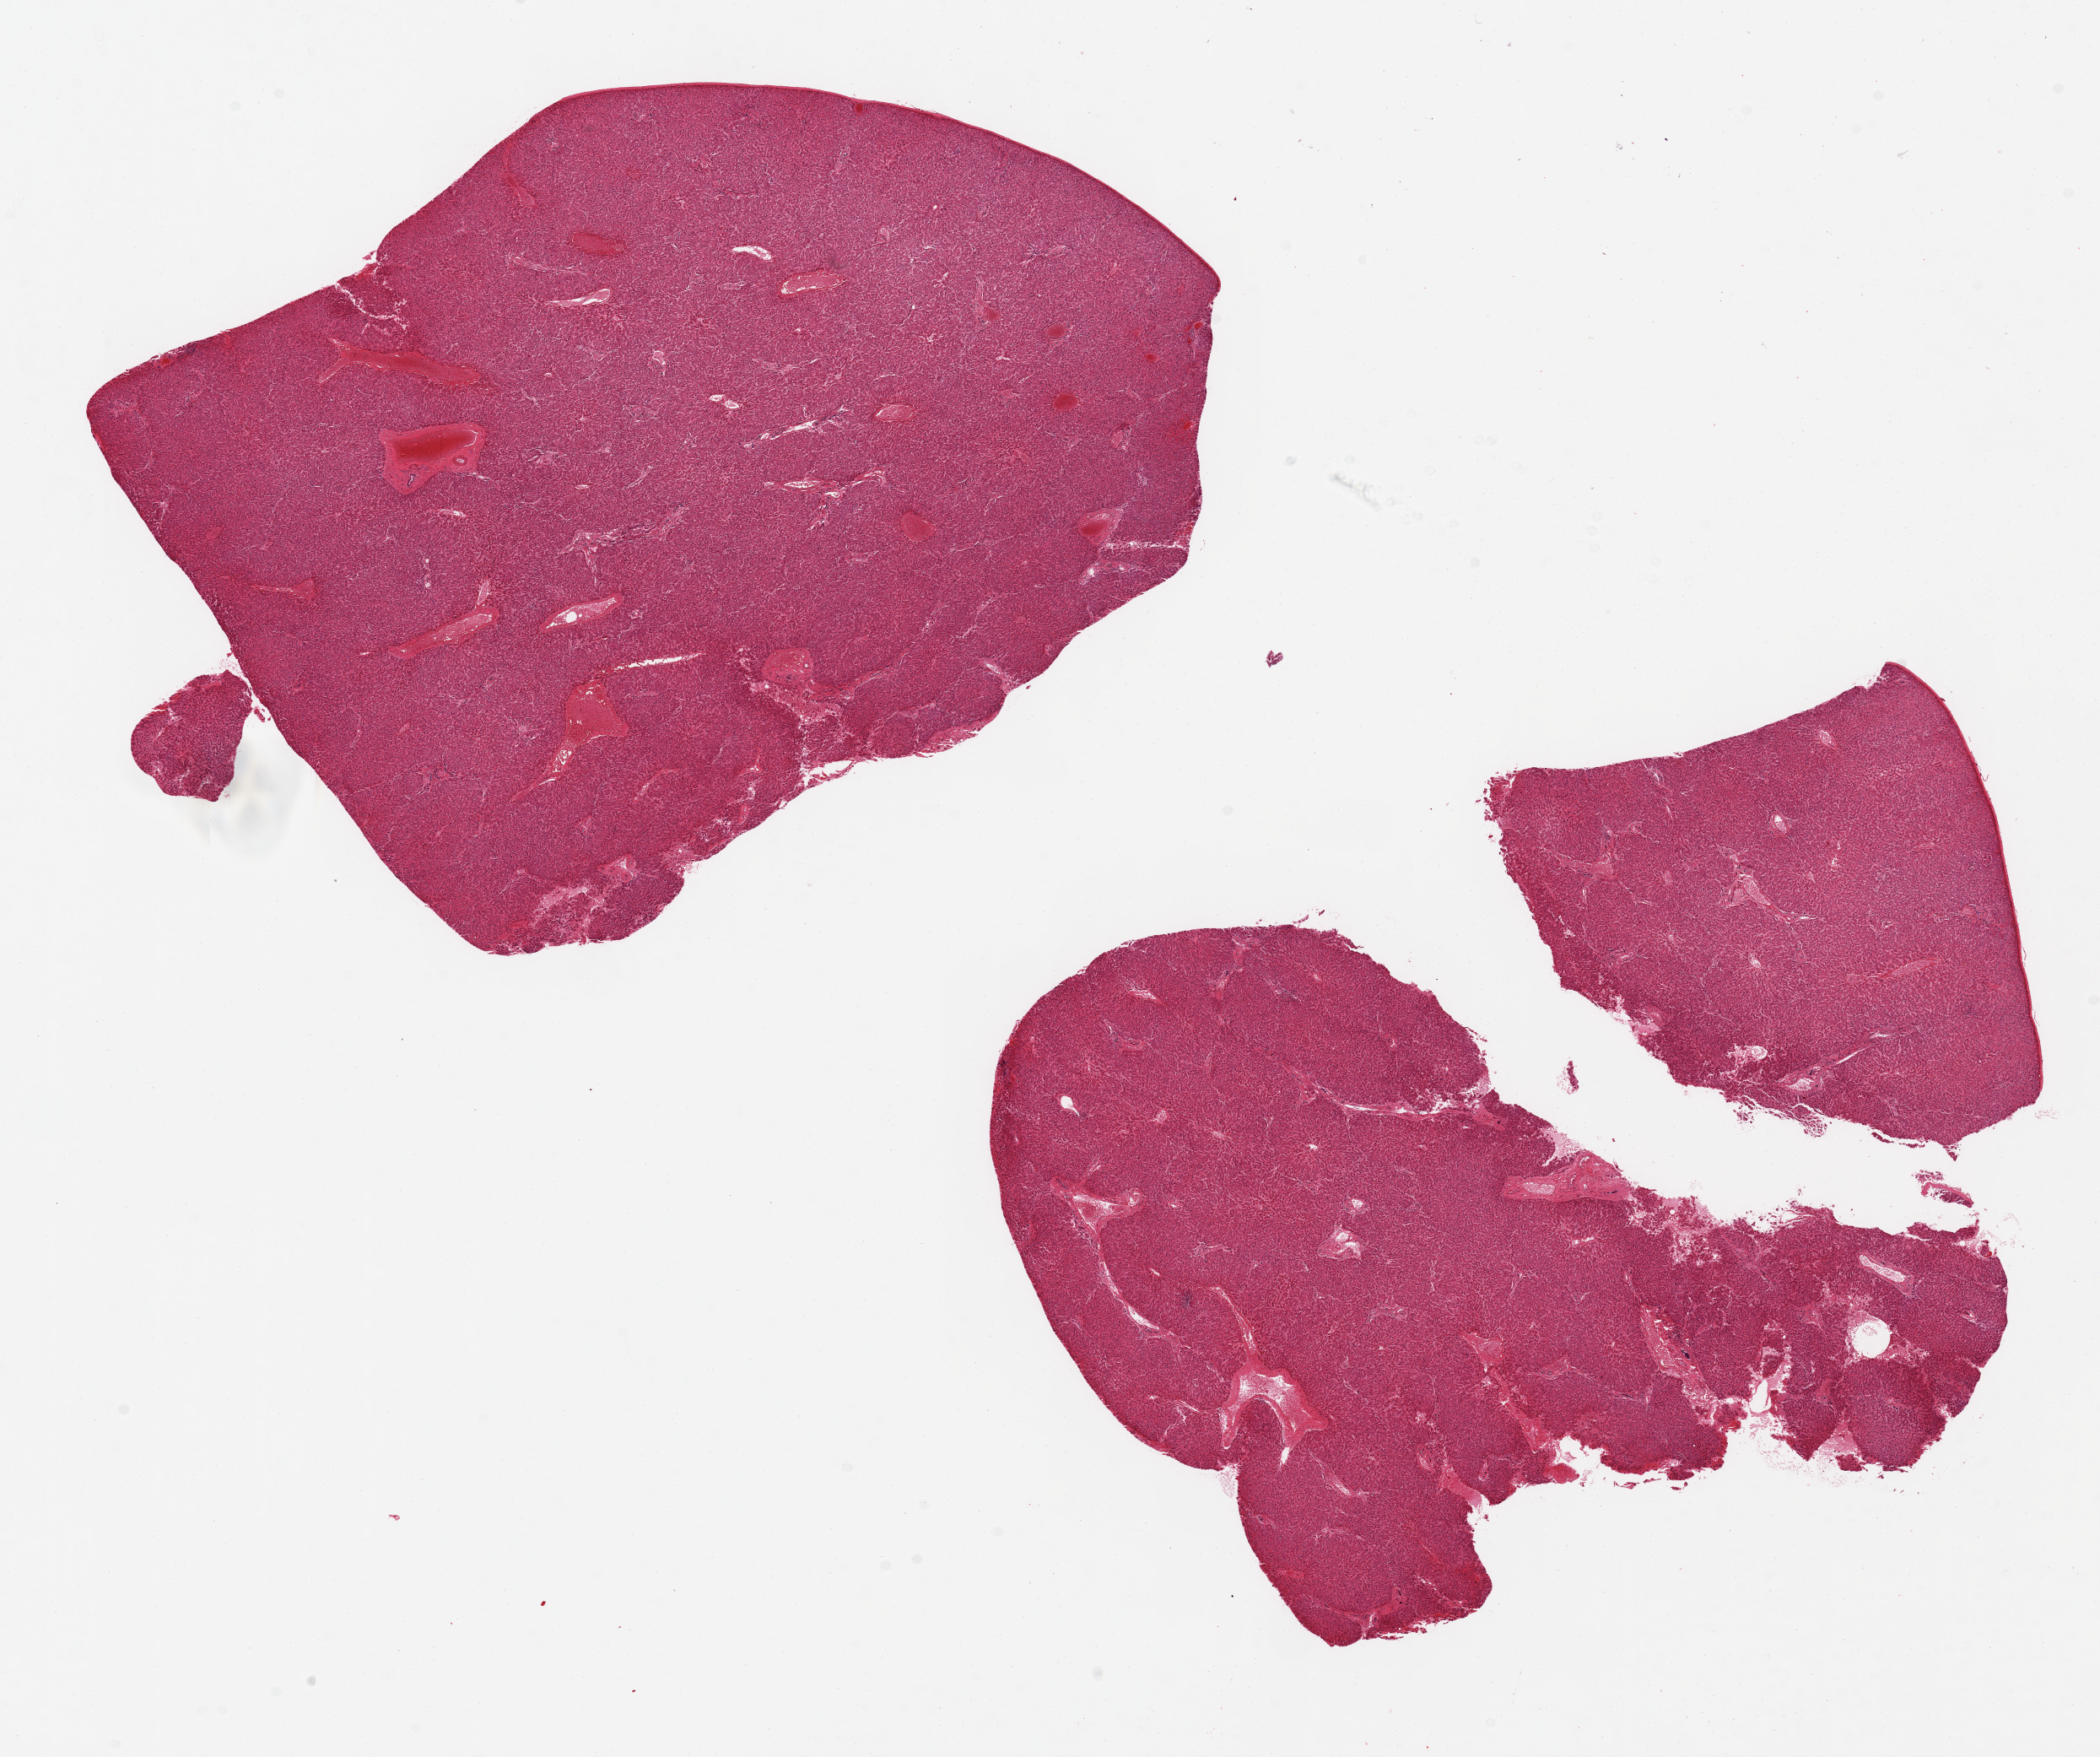
Whole-slide image, hematoxylin and eosin (H&E) stain, whole scanned area (about 19.7 x 16.5 mm, acquisition: 20x scan) shown as a low-resolution overview, PAXgene-fixed, paraffin-embedded tissue, section of liver (target tissue), donor tissue sample. Male donor.
Review note (as recorded): 2 pieces ~9.5x7 mm; 1 broken apart; good morphology.